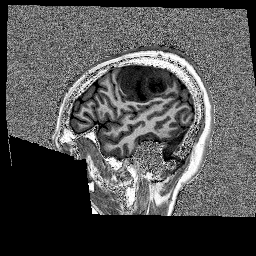
Brain MRI from a brain-tumour surgery series, one sagittal slice. Position 40 of 176 along the scan axis. 1 mm slice thickness. 256 × 256 image matrix, field of view 256 × 256 mm. Case-level facts recorded for this patient, not image findings: histopathology: Glioblastoma; WHO grade: 4; IDH mutation: no; tumour location: Left Frontal.
Outlined on this slice (manually delineated by an expert):
- tumour: bounding box [x1, y1, x2, y2] px = [118, 64, 175, 101]